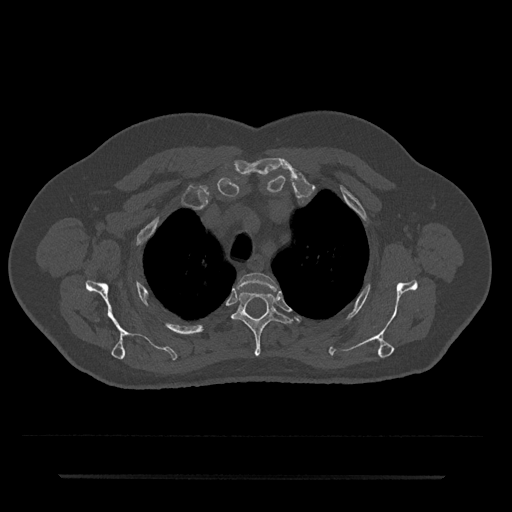
CT including the spine, one axial slice. Slice 571 of 797 in the series (ordered by position). Reconstruction kernel Br40s/3. Bone window (W 1800 / L 400 HU). 0.5 mm slice thickness. 512 × 512 image matrix, field of view 437 × 437 mm. Patient: male, 69 years. From the clinical record (not read from this slice): primary cancer: prostate.
Annotated regions visible in this slice (semi-automatic segmentation, software-assisted and operator-edited):
- T2 vertebra: bounding box <238,273,277,290> (left, top, right, bottom; pixels)
- T3 vertebra: <232,291,291,357>